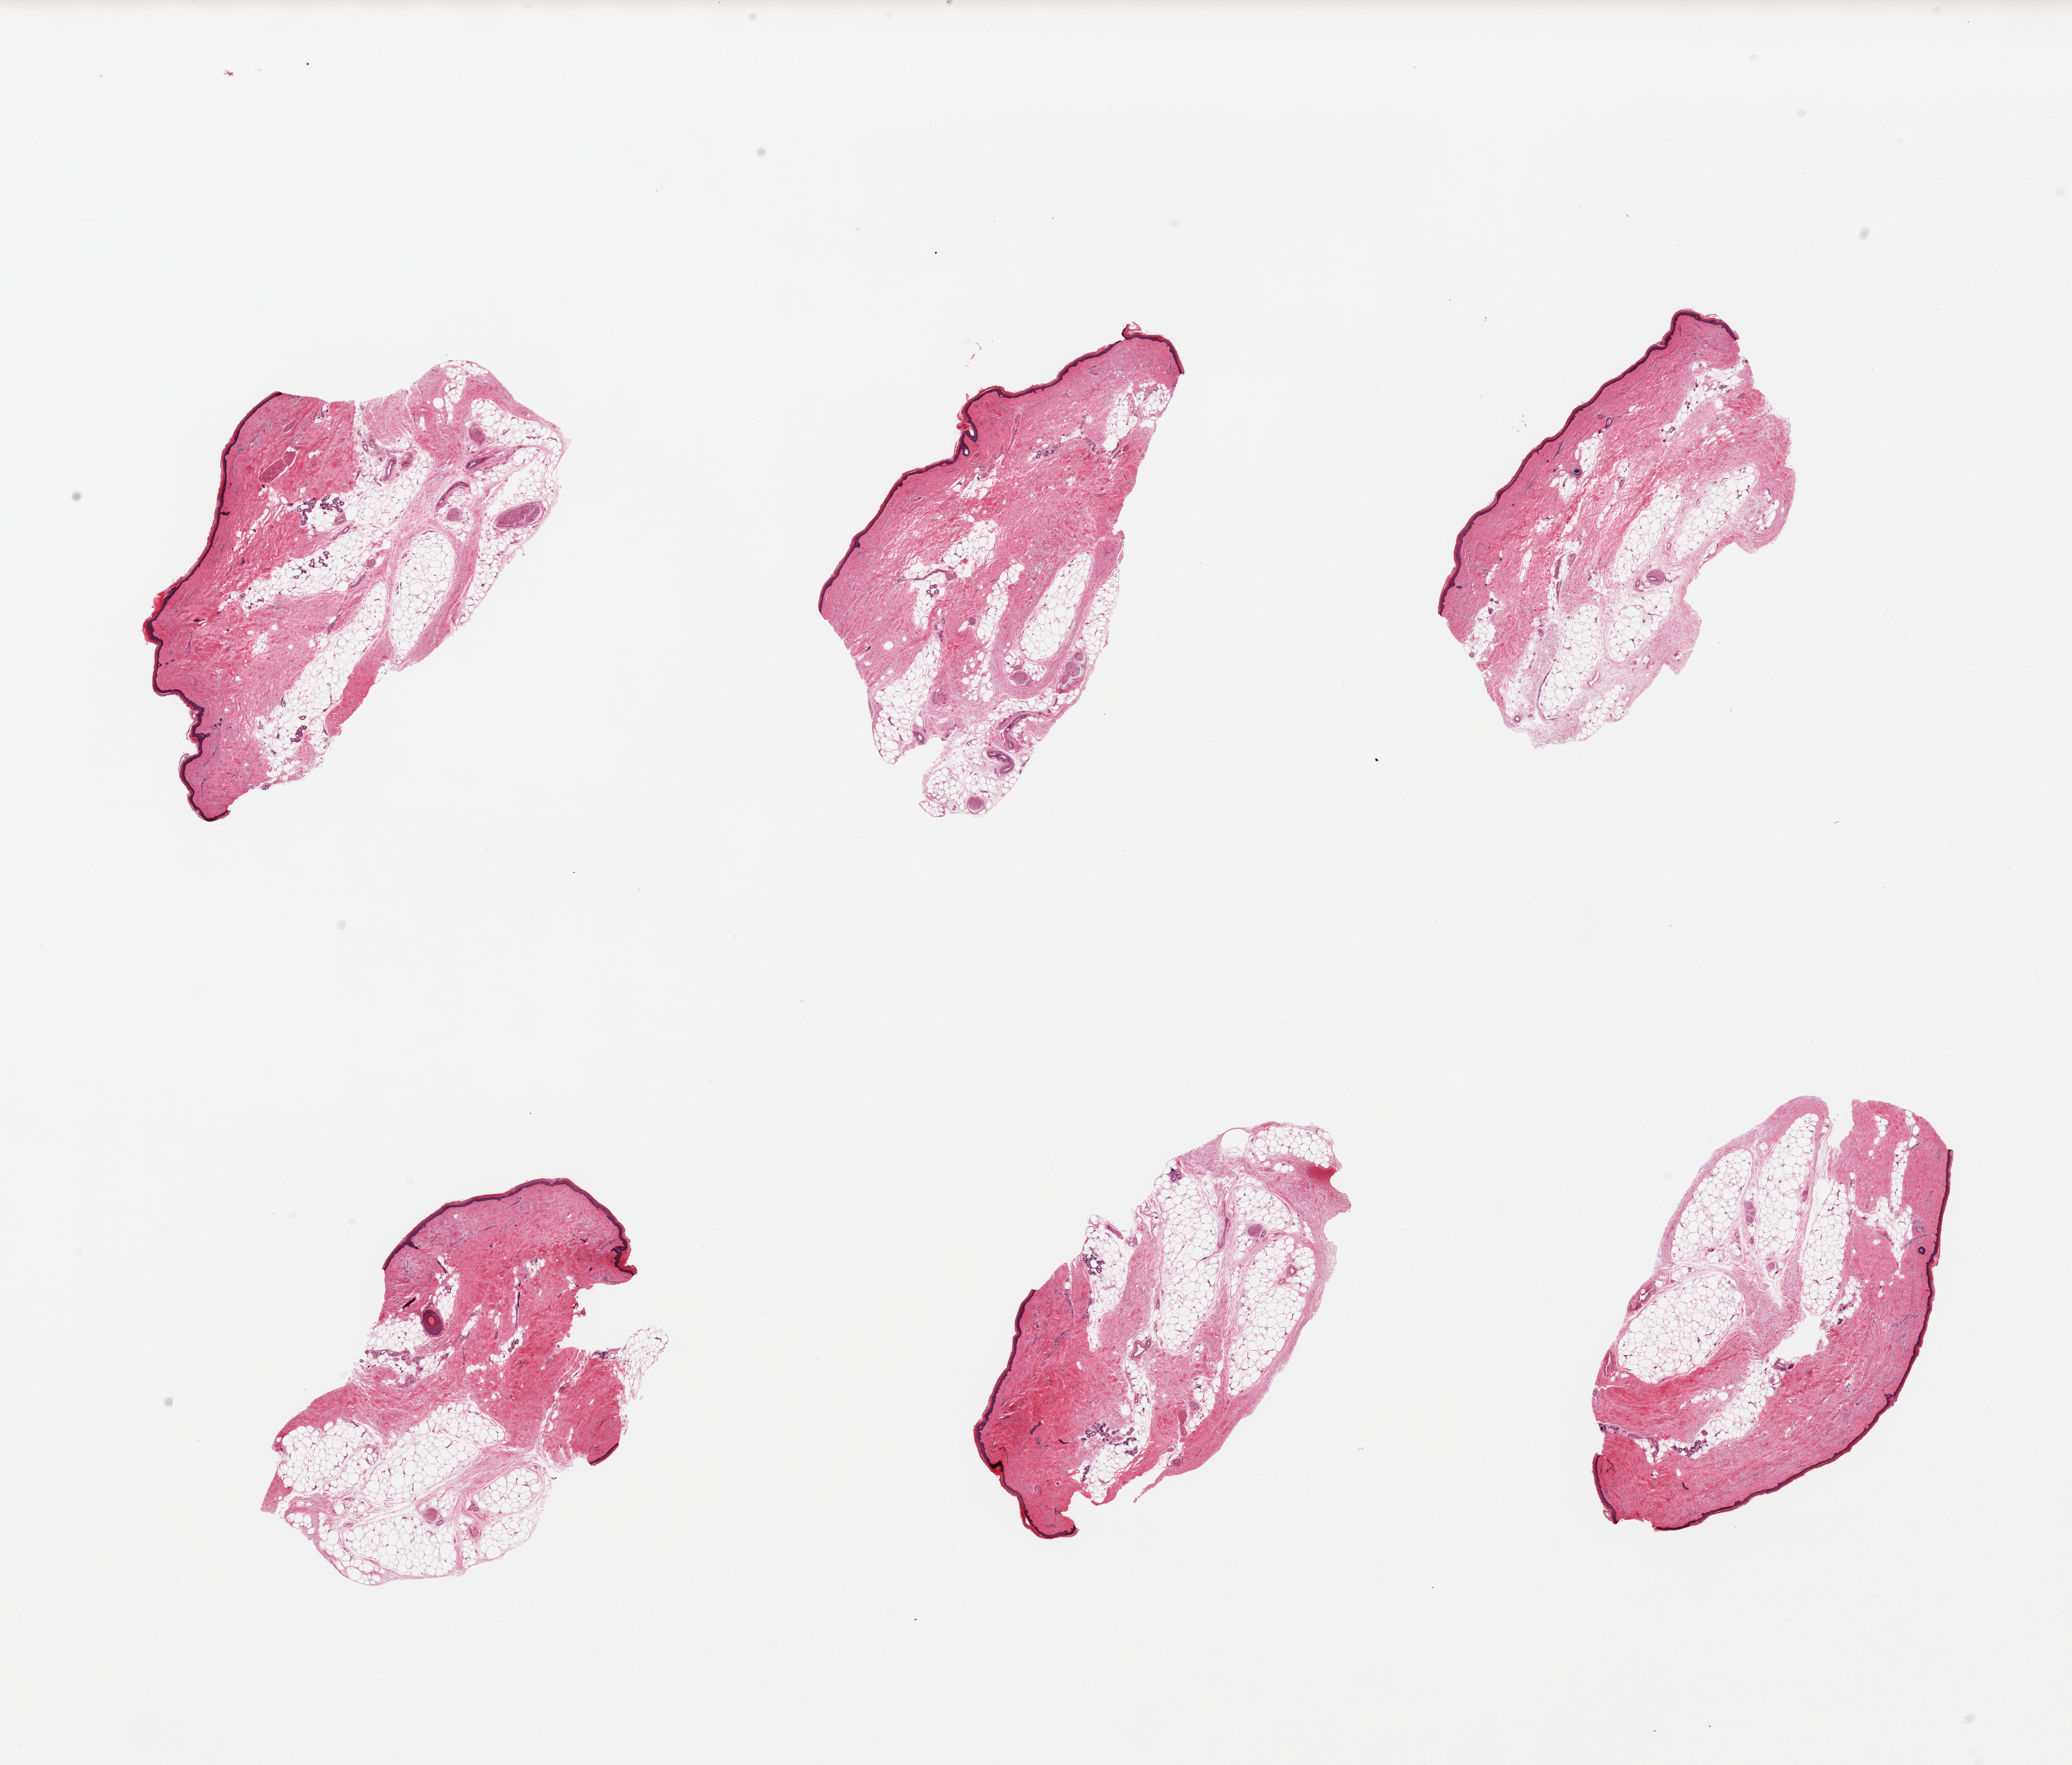
H&E whole-slide image — a low-resolution overview of the entire scanned area, about 23.6 x 20.1 mm. PAXgene-fixed, paraffin-embedded tissue. Section of skin of lower leg (target tissue). Donor tissue sample.
Review note (as recorded): 6 pieces, adherent fat up to 2 mm some sections, squamous epithelium is ~20-30 microns.